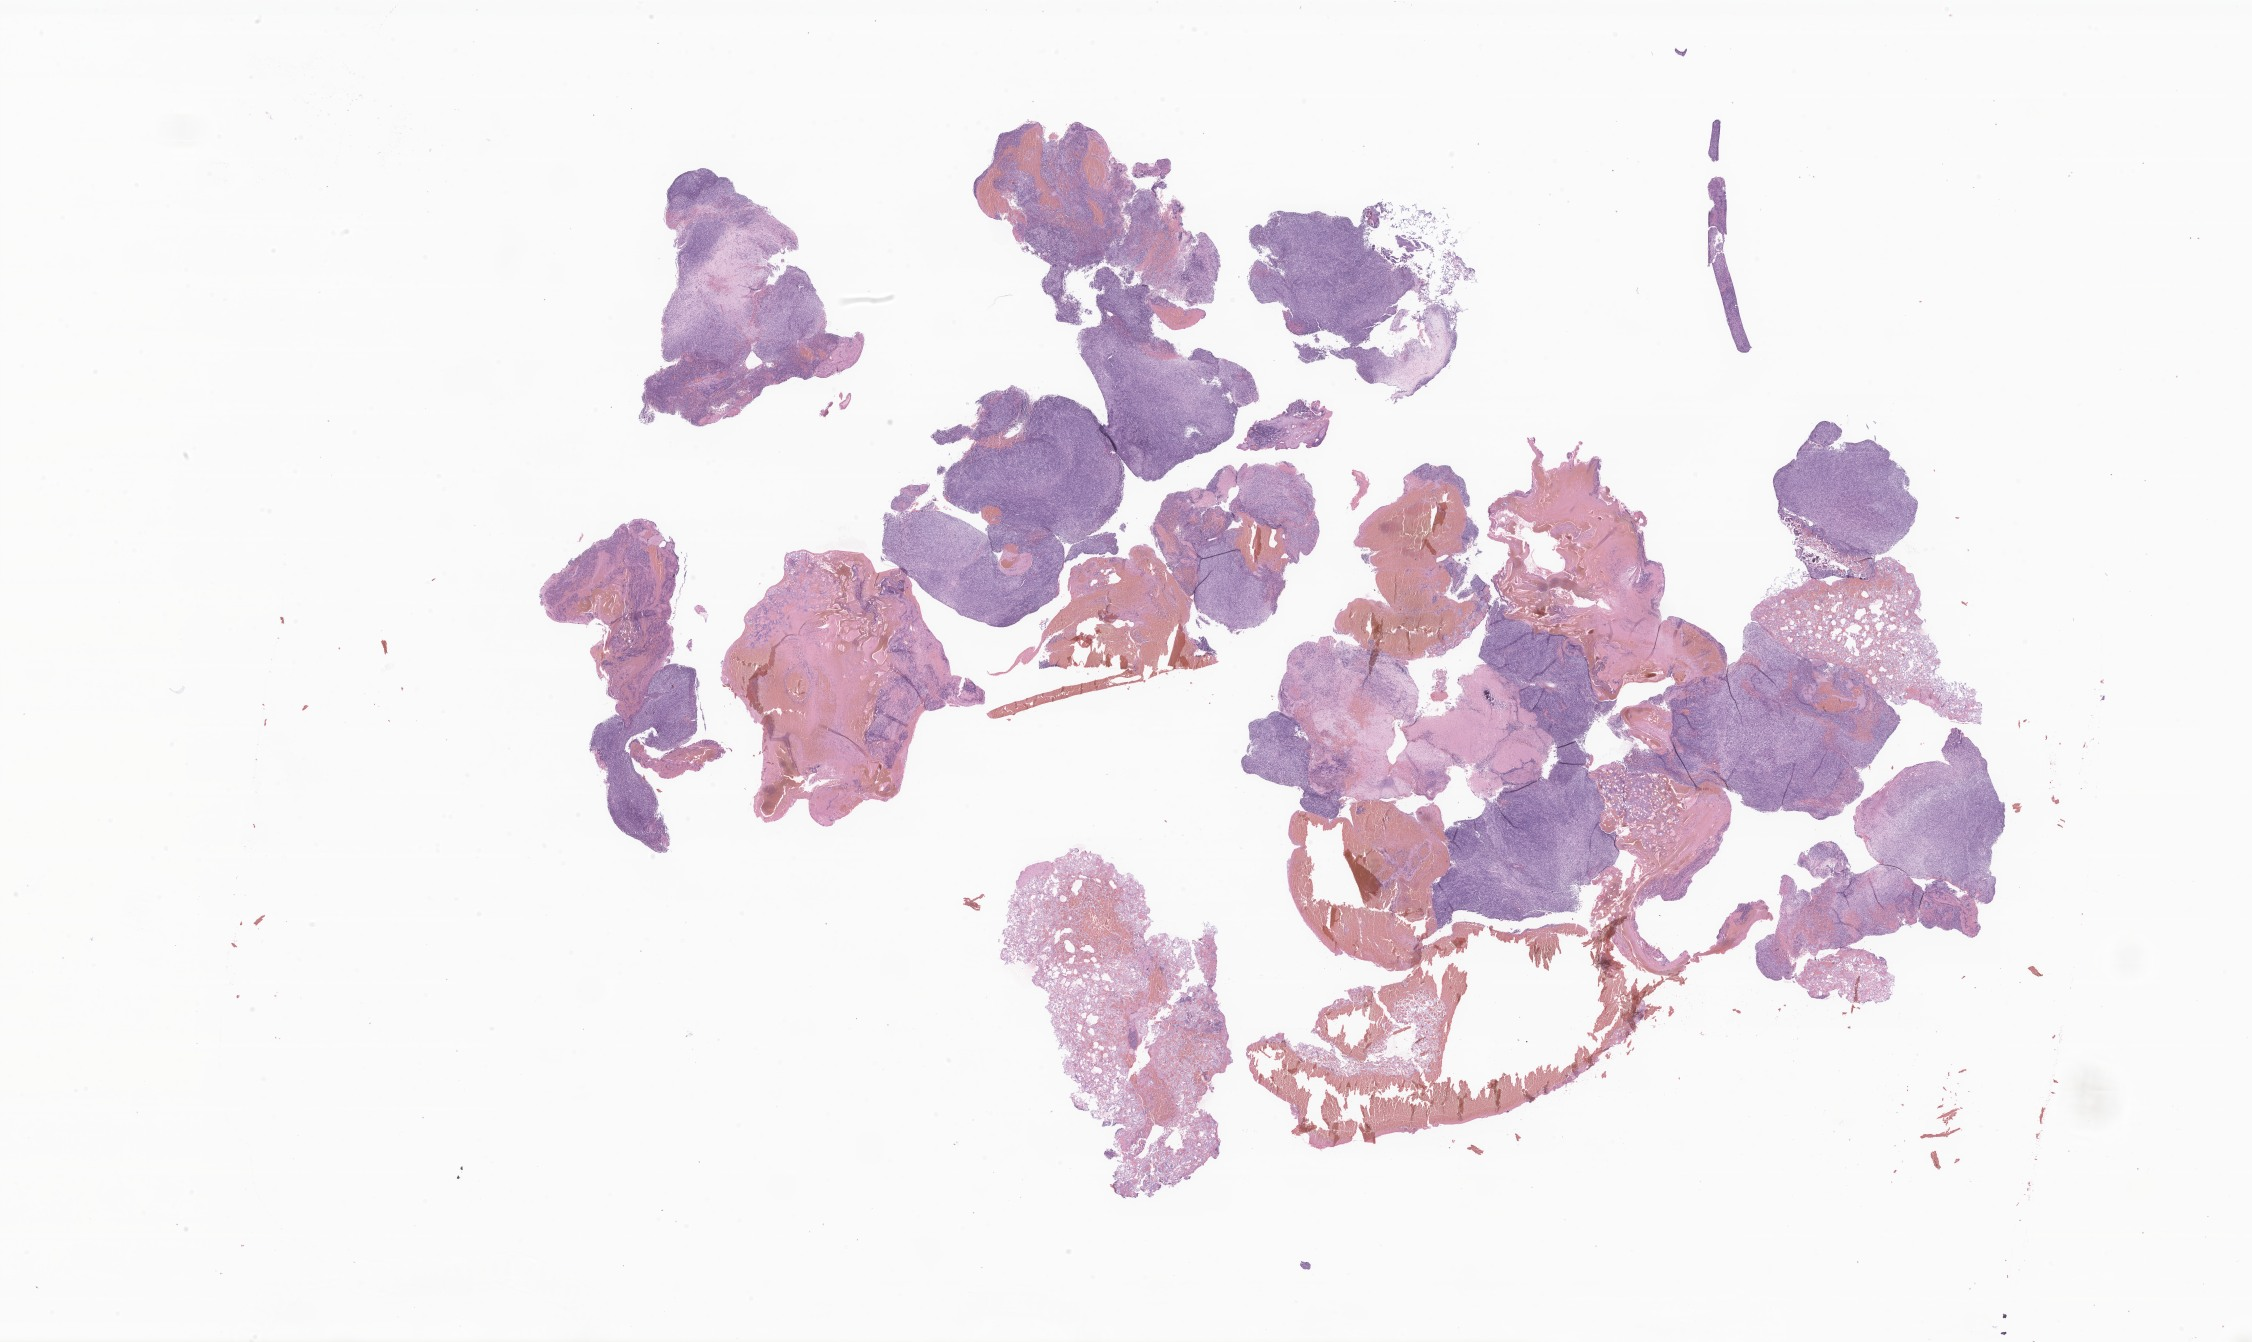
H&E whole-slide image of tumor tissue from the brain — shown as a low-resolution overview of the whole scanned area (about 38.0 x 22.6 mm), formalin-fixed, paraffin-embedded (FFPE) tissue. Patient: female, age 53 months (4 years 5 months).
Recorded diagnosis: Atypical teratoid/rhabdoid tumor.